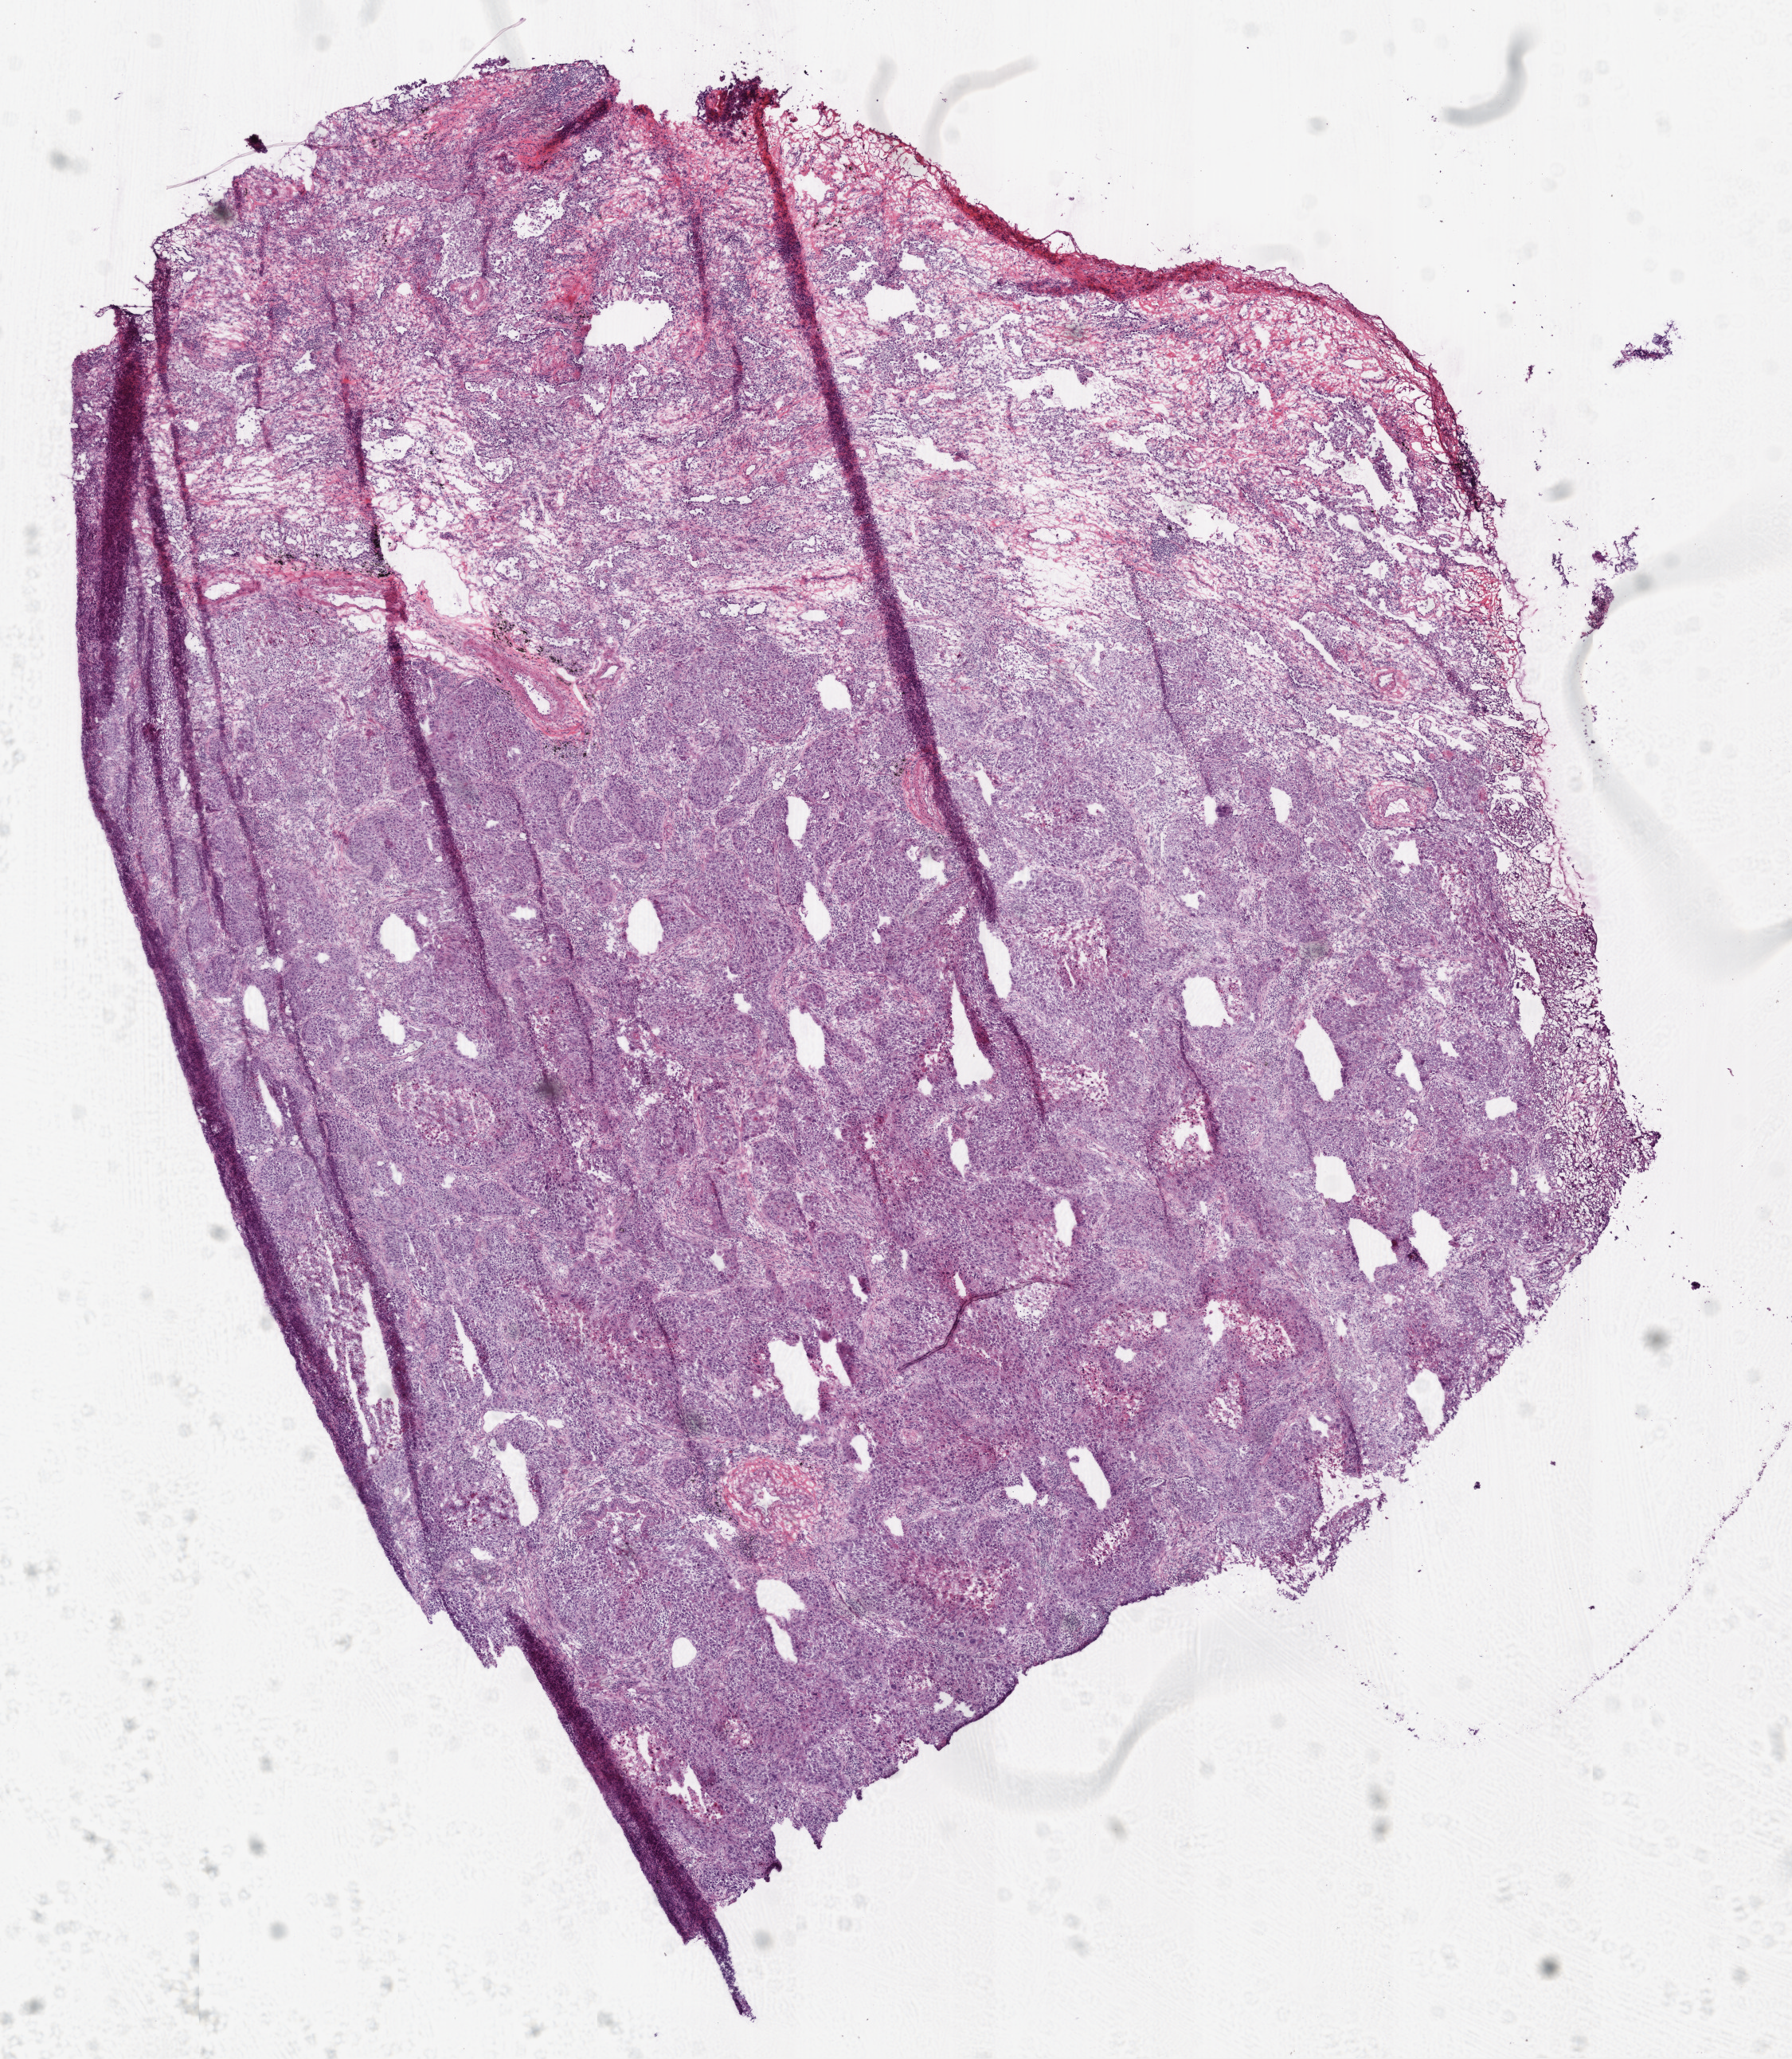
Whole-slide histology image, H&E — a low-resolution overview of the entire scanned area, about 9.0 x 10.4 mm (from a 20x scan). Frozen section from the bottom of the tissue portion. Lung, primary tumour sample. Patient: male, age at initial diagnosis 69 years. Composition of this section per pathologist review: tumour cells 63%, tumour nuclei 60%, normal cells 30%, stromal cells 5%, necrosis 2%.
* laterality: left
* diagnosis: Squamous cell carcinoma, NOS (lower lobe, lung)
* AJCC pathologic stage: IB (6th edition)